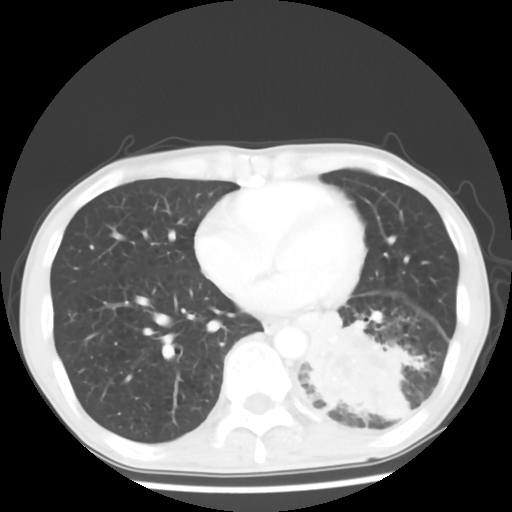
Chest CT, one axial slice; position 23 of 64 along the scan axis; 120 kVp; lung window (W 1500 / L -600 HU); 5 mm slice thickness; 512 × 512 image matrix, field of view 313 × 313 mm. Patient: male, 68 years. Case-level facts recorded for this patient, not image findings: clinical TNM (as recorded): T4 N0 M0.
Structures marked on this image (bounding box drawn by a radiologist):
- lung tumour (recorded histology: squamous cell carcinoma): bounding box [x1, y1, x2, y2] px = [304, 309, 413, 433]